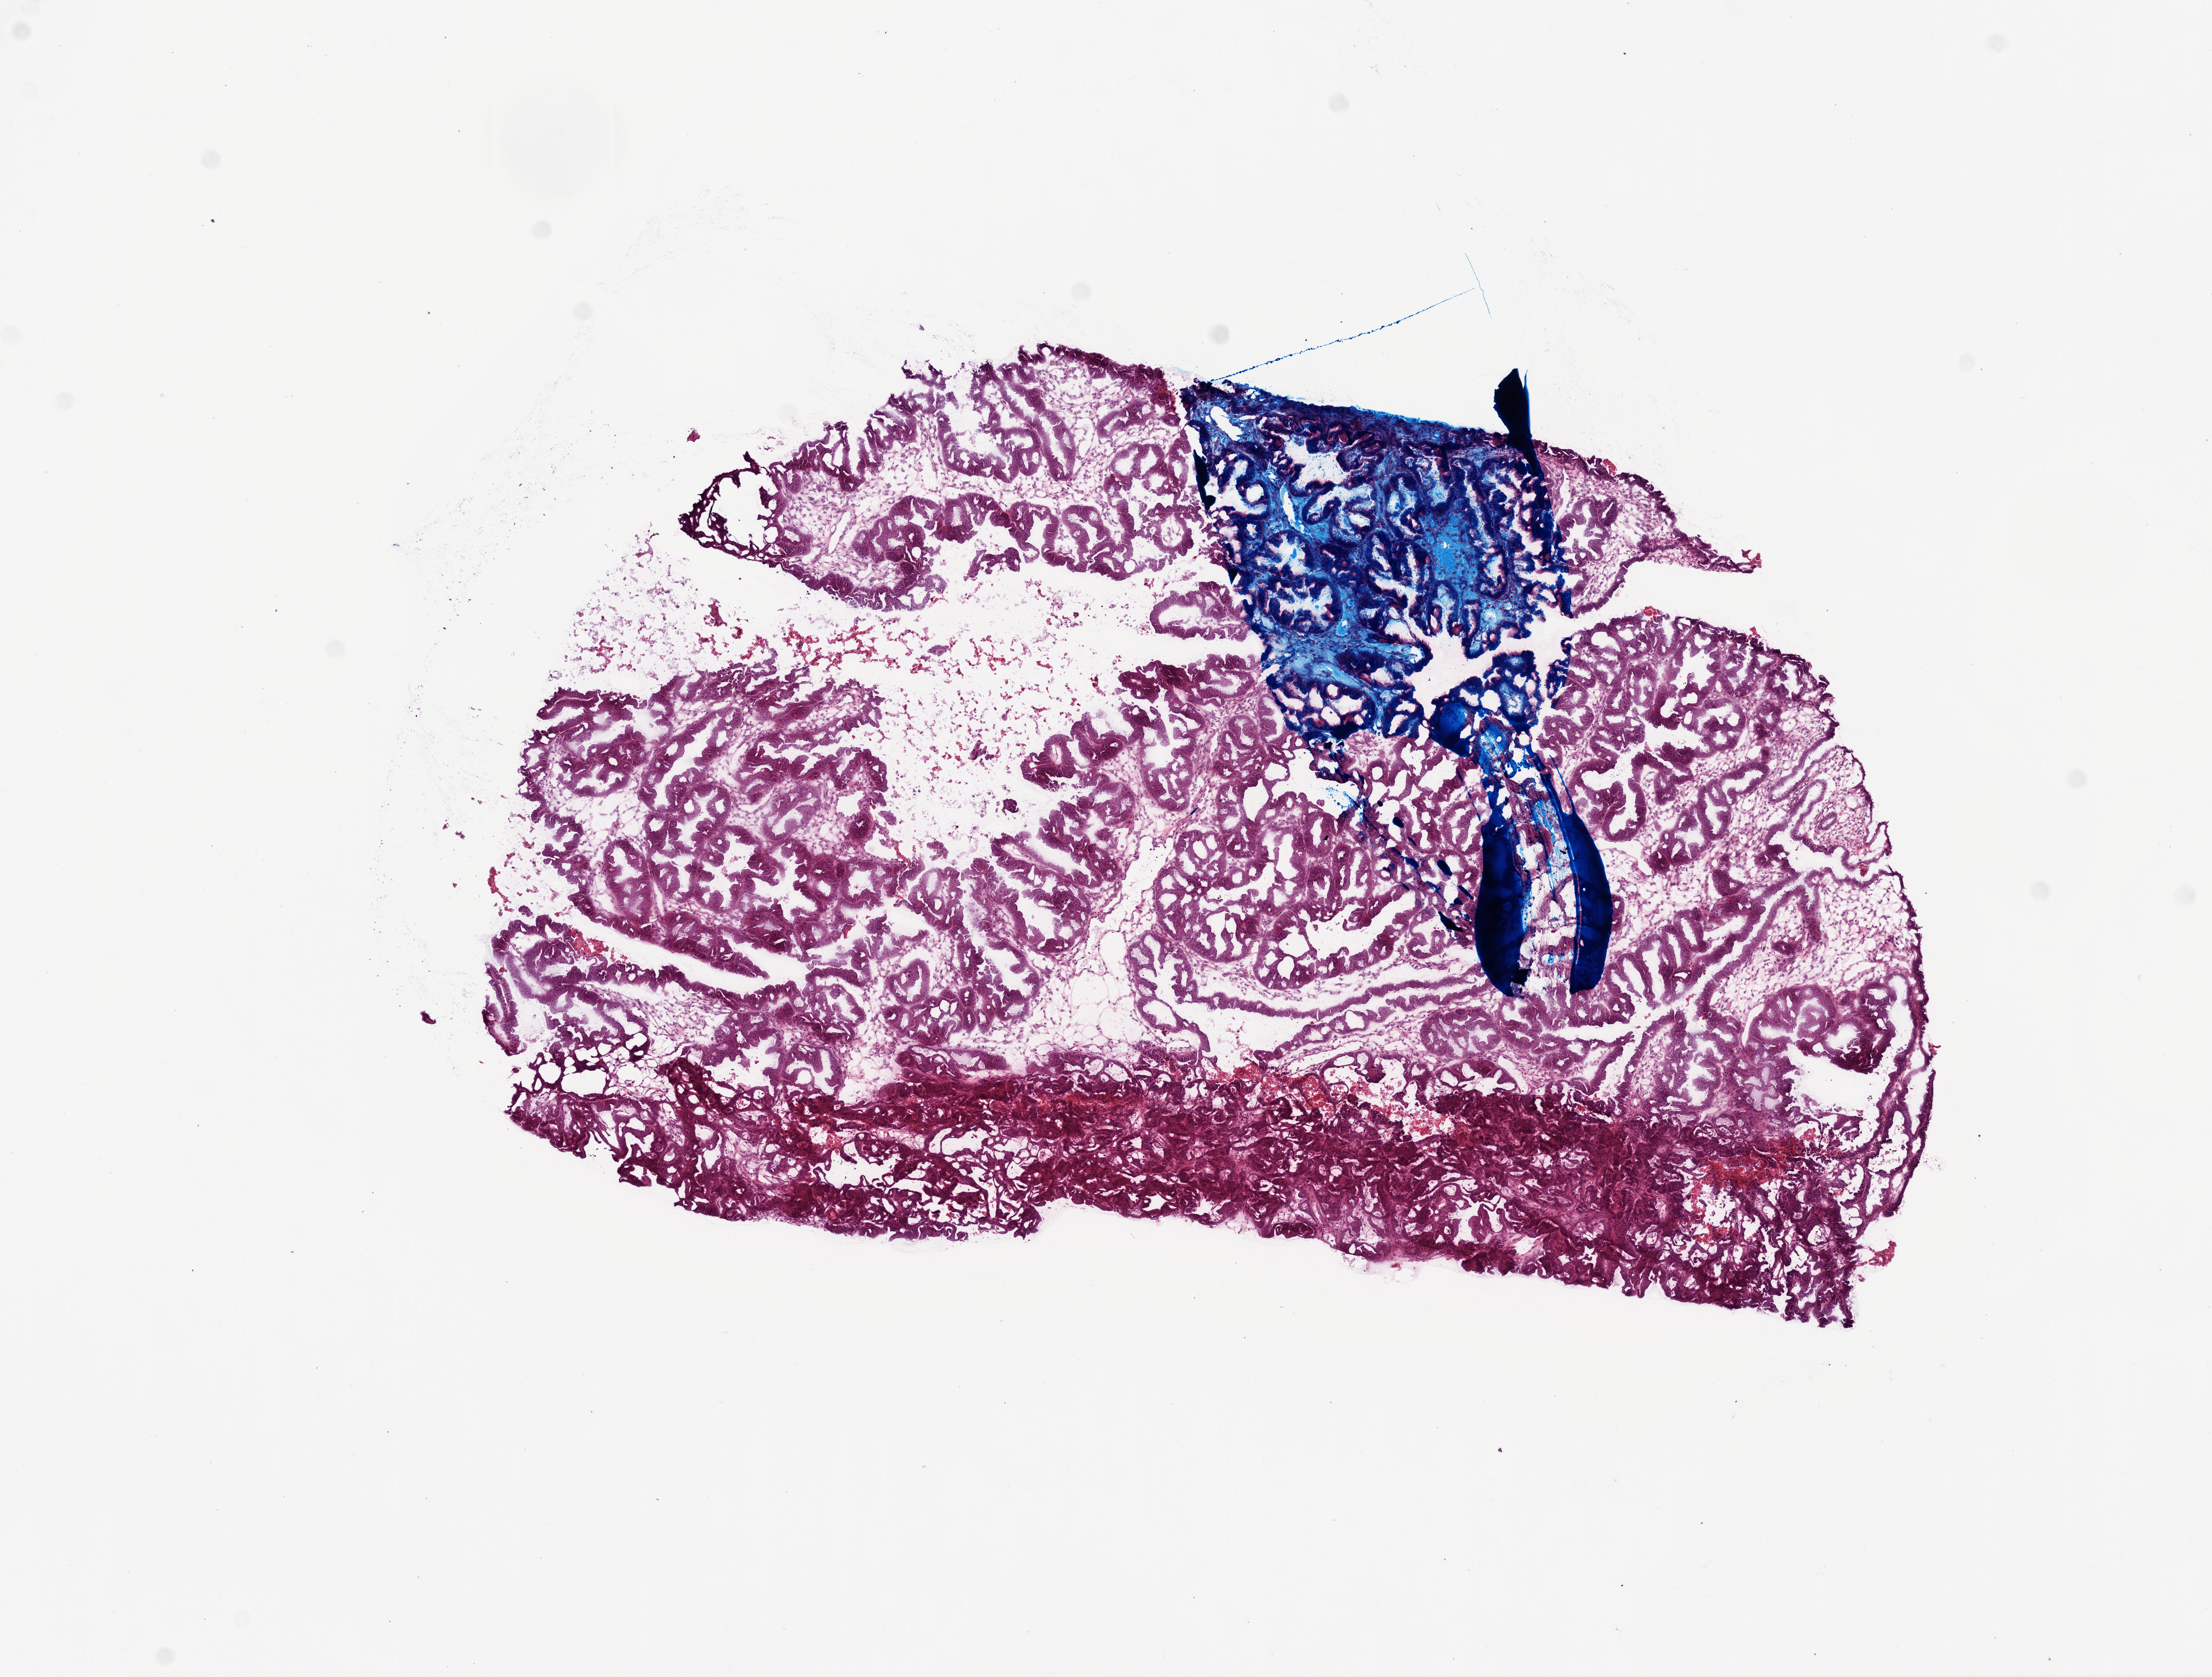
Digitized Hematoxylin and eosin (H&E) stained tissue section (whole slide), shown as a low-resolution overview of the whole scanned area (about 8.7 x 6.6 mm, slide scanned at 20x); frozen section from the top of the tissue portion; ovary, primary tumour sample. Female, age 50 years at initial diagnosis. Histologic grade: G3 (poorly differentiated). Slide review estimates, as recorded: tumour cells 80%, tumour nuclei 80%, normal cells 5%, stromal cells 15%, necrosis 0%.
• histologic diagnosis: Serous cystadenocarcinoma, NOS
• FIGO stage: IIIC